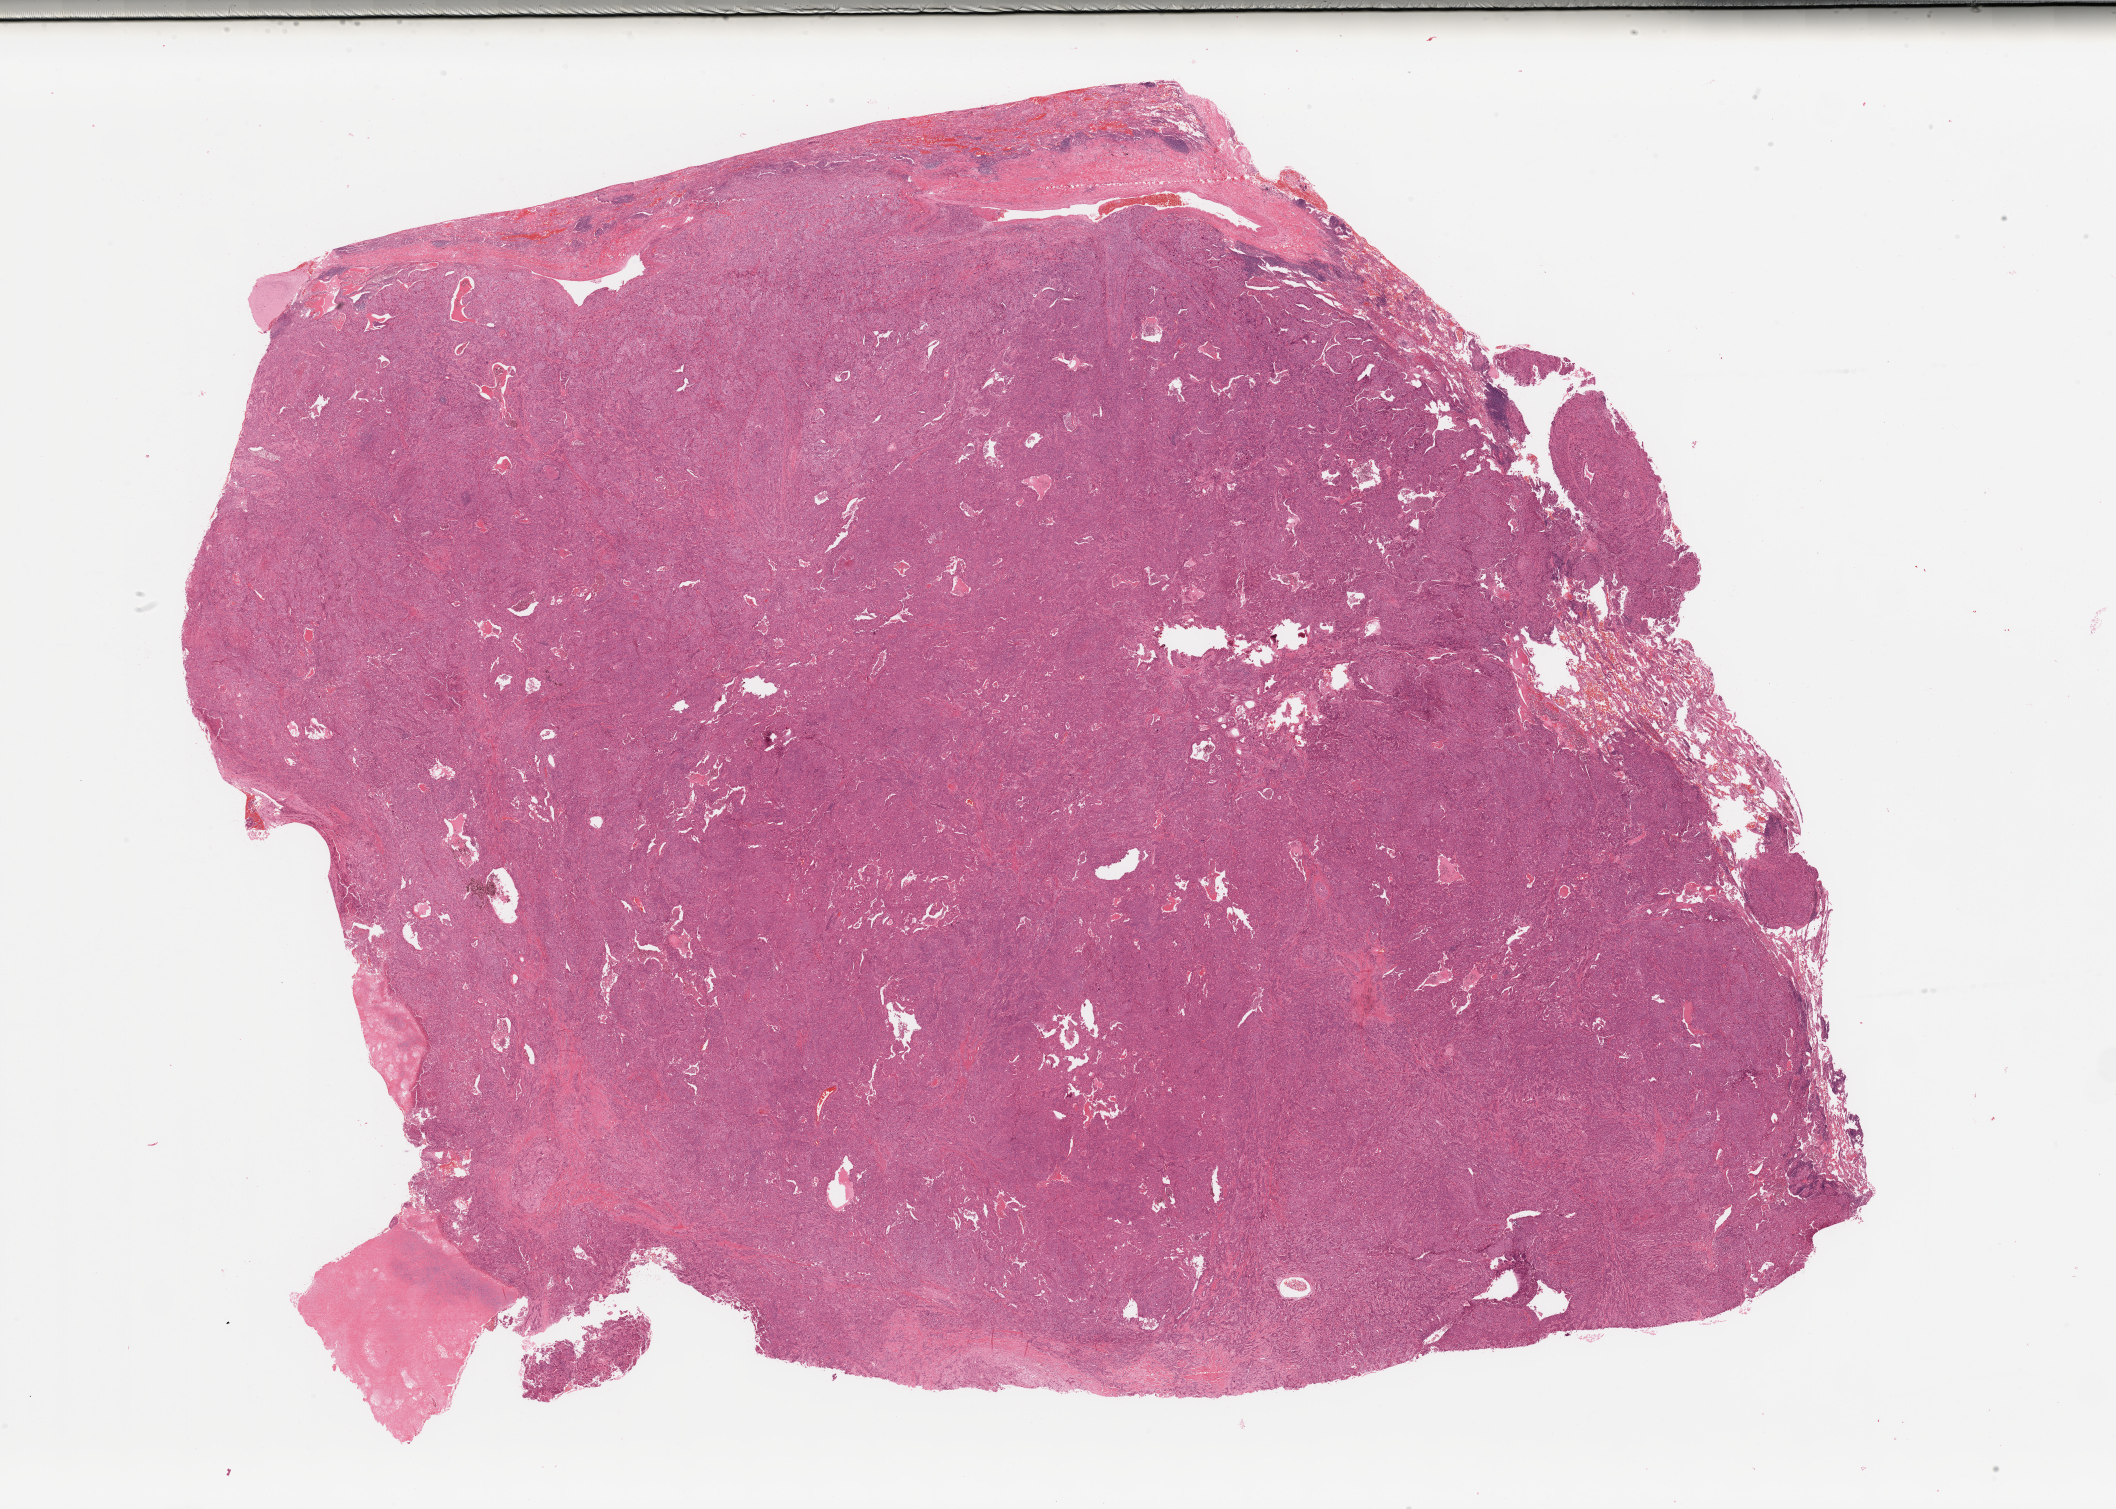
Digitized H&E tissue section (whole slide), a low-resolution overview of the entire scanned area, about 33.5 x 23.9 mm; lung, tissue type not recorded.
• patient diagnosis (cohort enrolment): lung adenocarcinoma (lung)